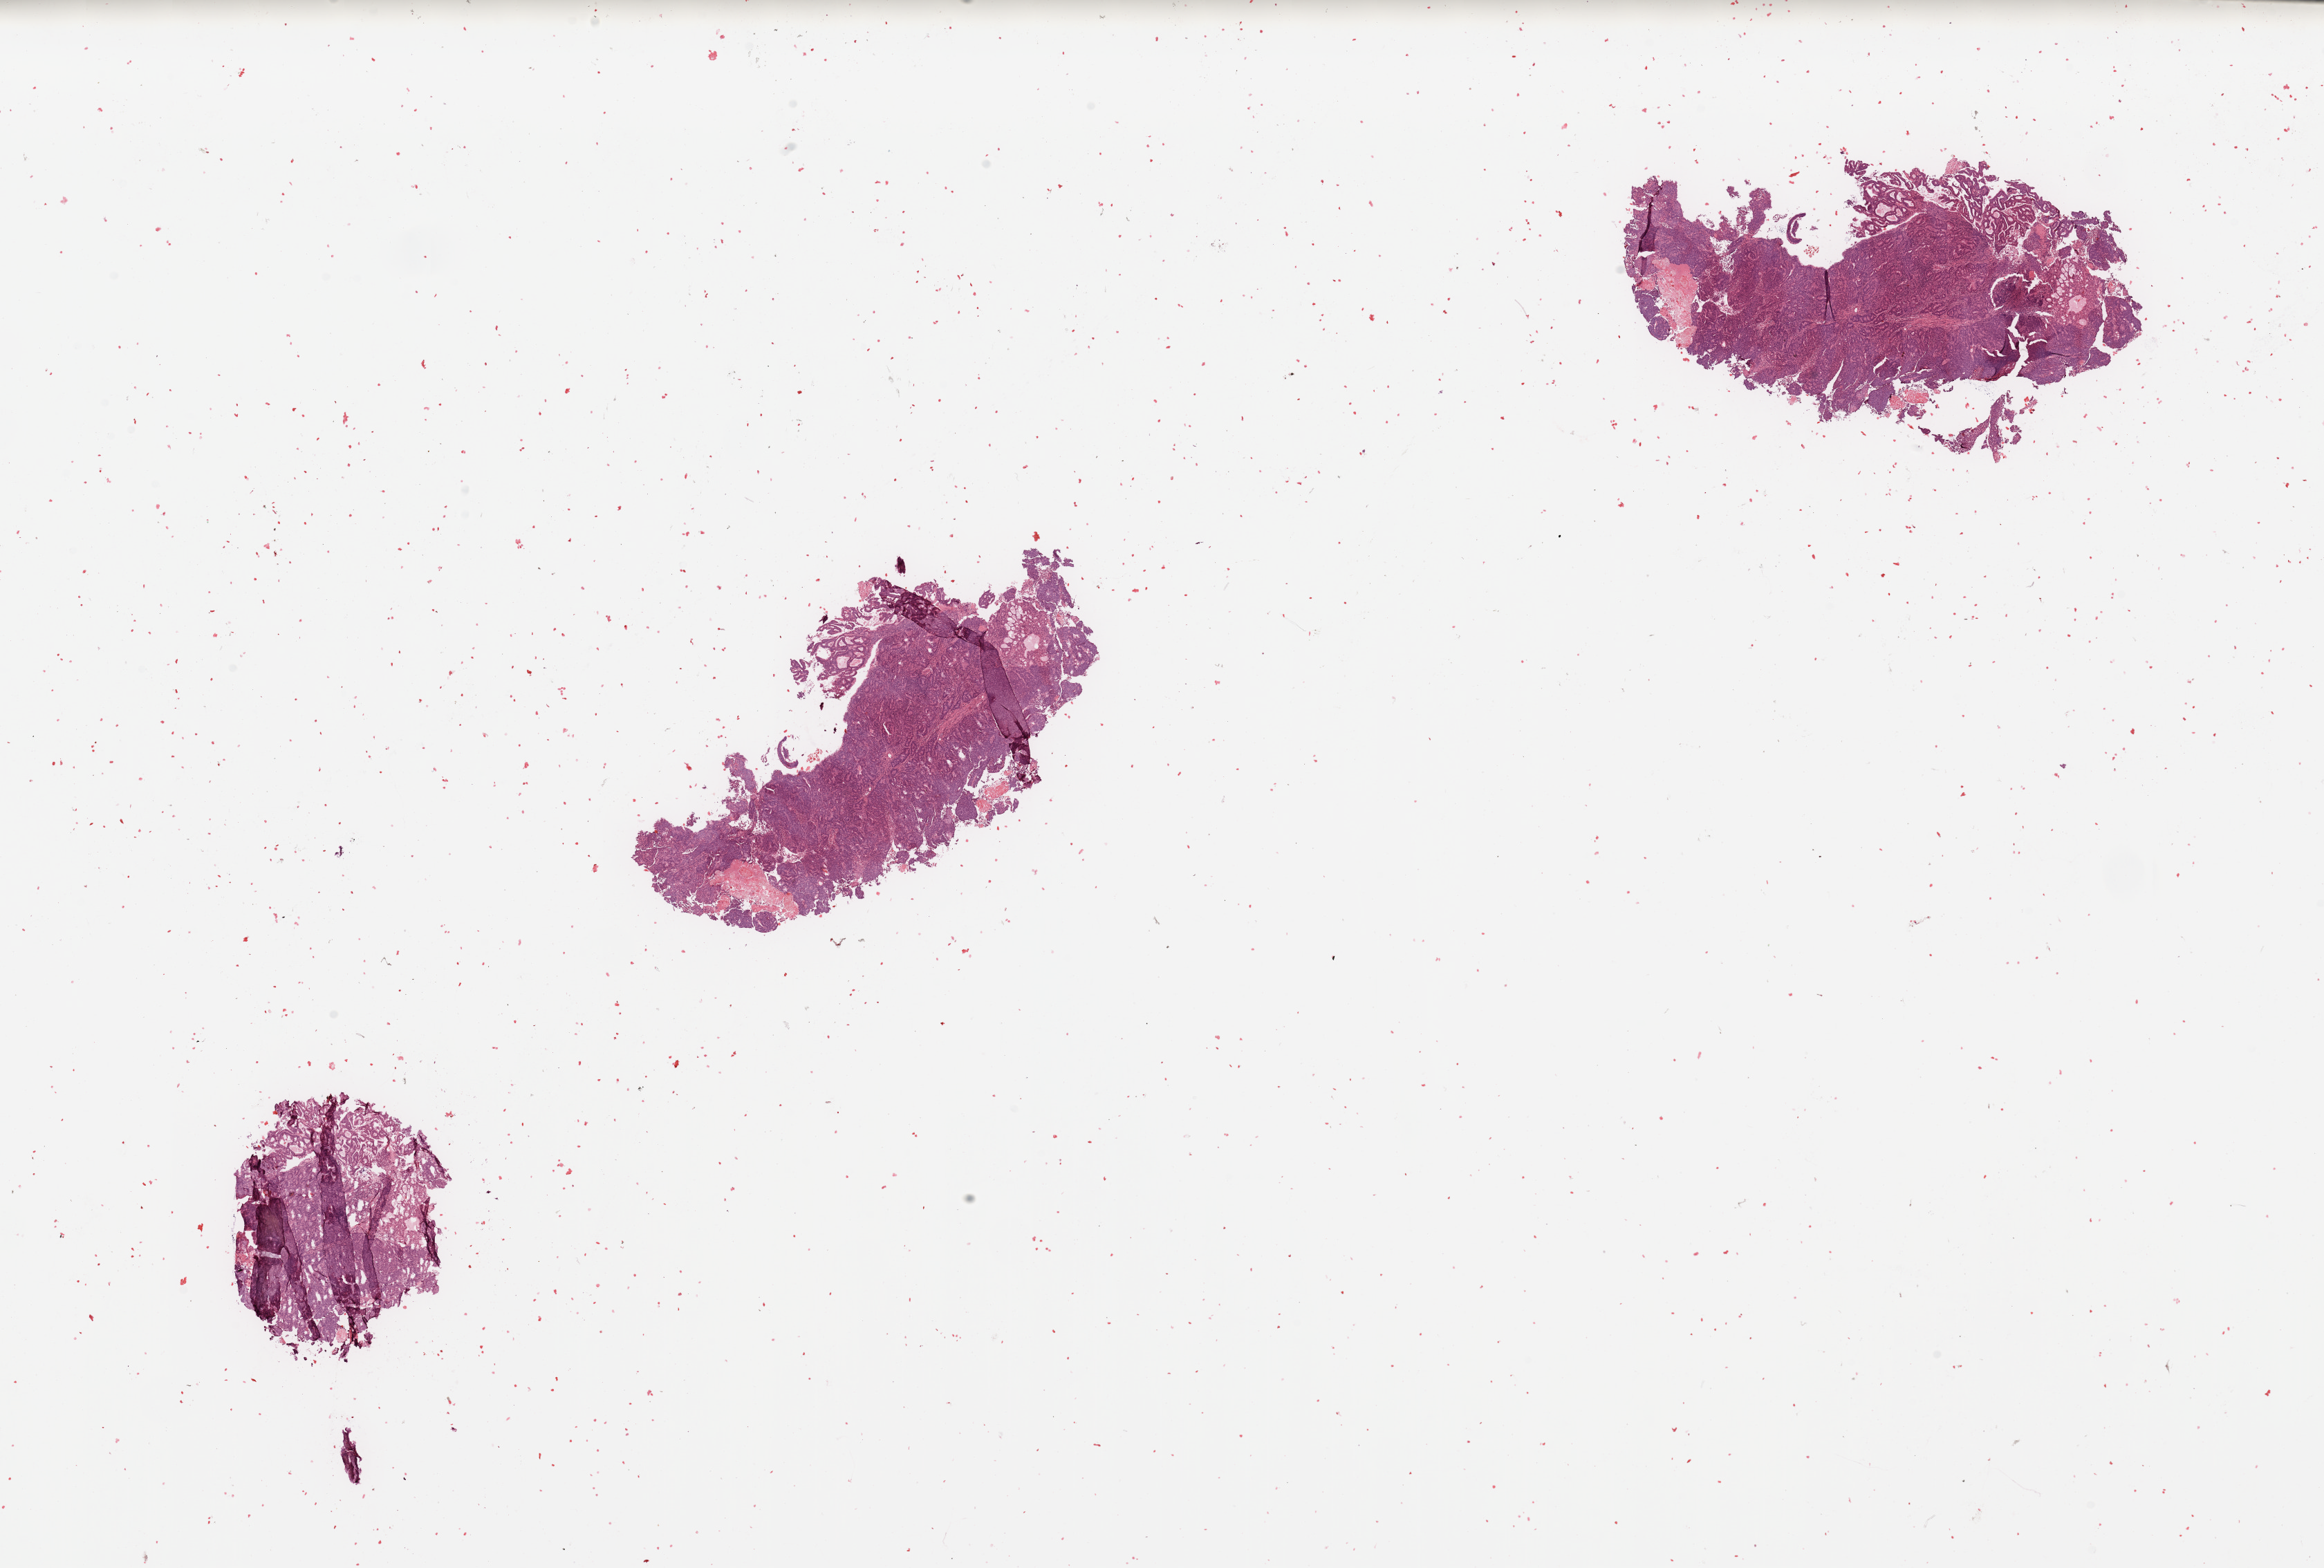
Whole-slide histology image, H&E-stained, a low-resolution overview of the entire scanned area, about 26.6 x 17.9 mm; tumour tissue sample, sampled site: uterus. Female, 65 y/o. Histologic grade: G2 (moderately differentiated). Pathologist review of this section (percent, as recorded): tumour nuclei 90%, necrosis 20%.
* AJCC pathologic stage: I
* primary tumour site (as recorded): anterior endometrium
* histologic diagnosis: Endometrioid adenocarcinoma, NOS